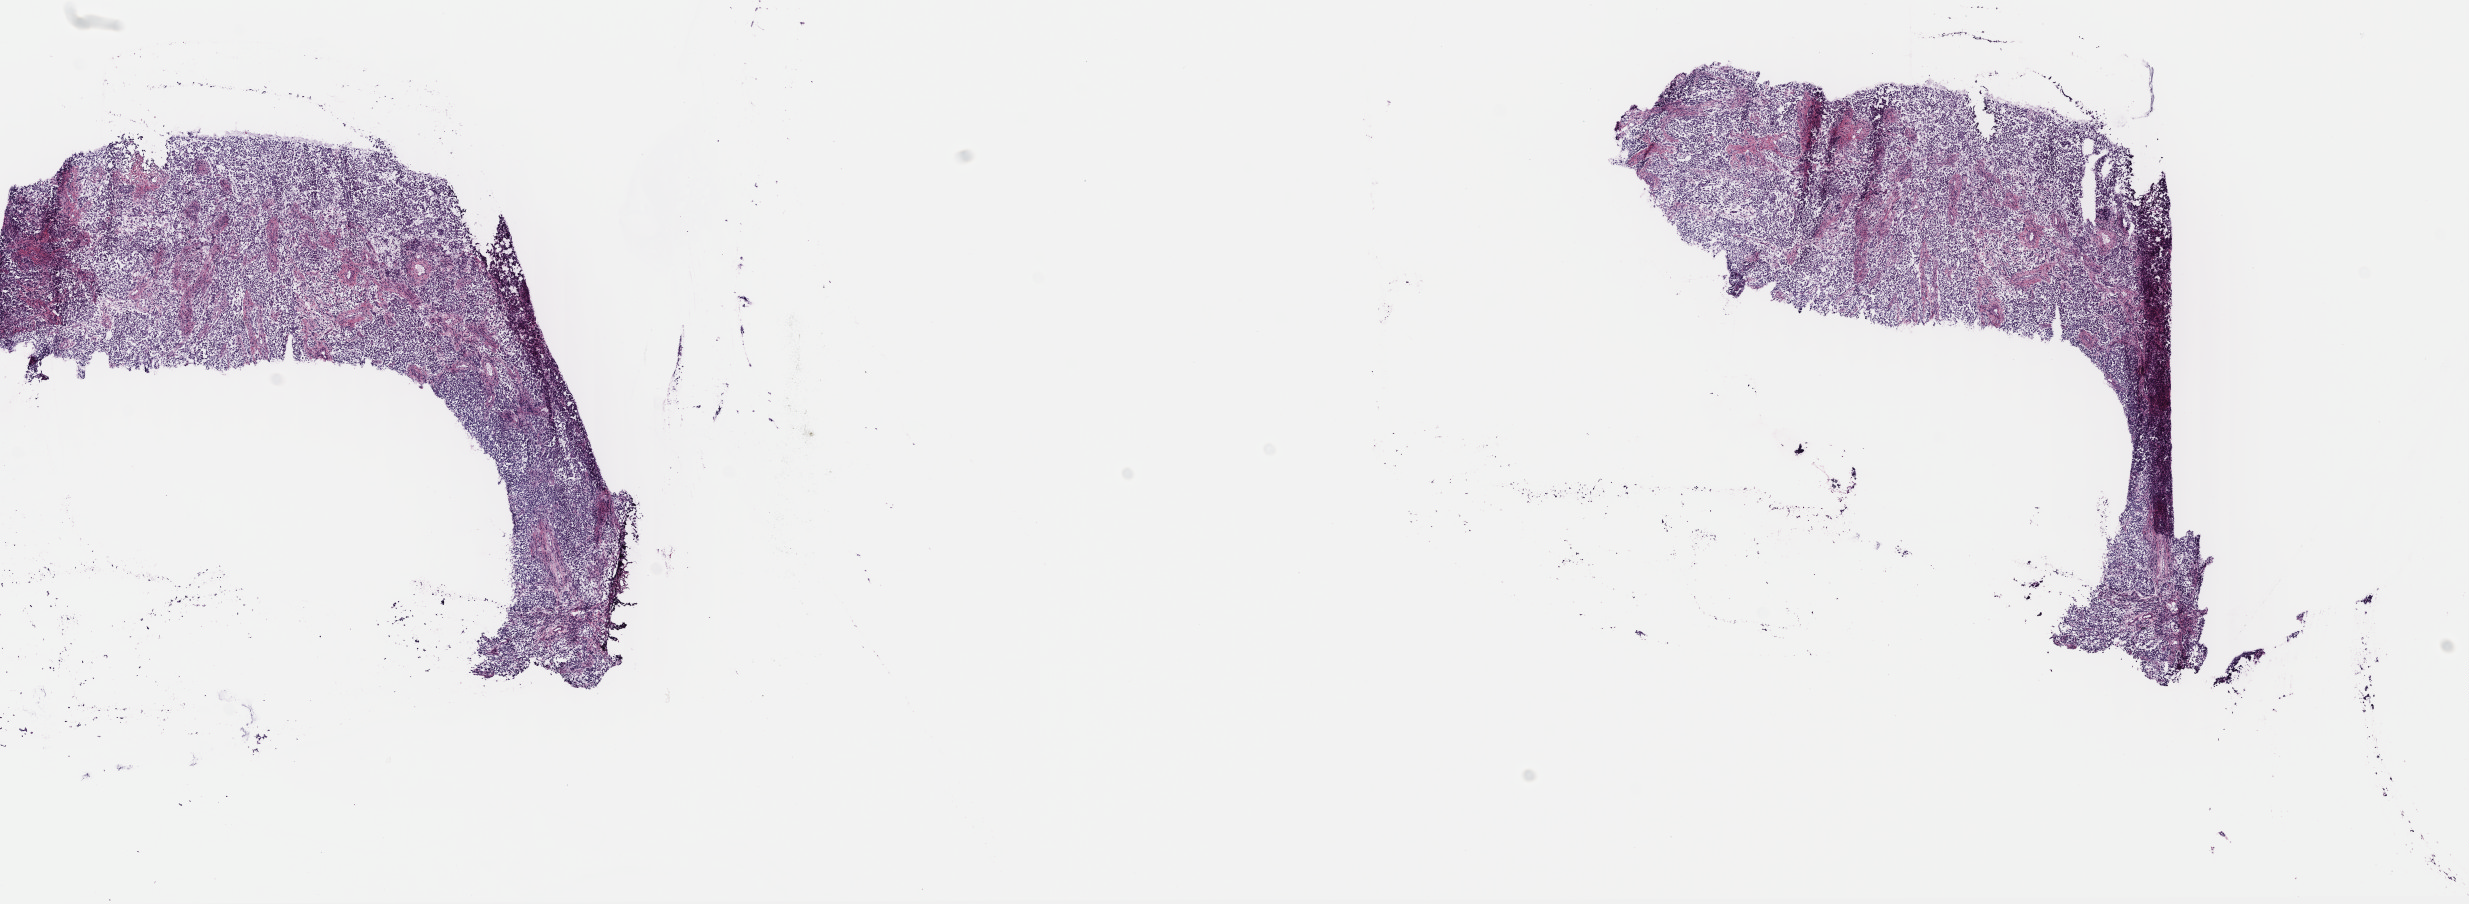
H&E whole-slide image, shown as a low-resolution overview of the whole scanned area (about 19.4 x 7.1 mm, from a 40x scan), frozen section from the top of the tissue portion, sample: primary tumour, cervix. Patient: female, age at initial diagnosis 34 years. Histologic grade: G3 (poorly differentiated). Slide review estimates, as recorded: tumour cells 80%, tumour nuclei 80%, normal cells 10%, stromal cells 5%, necrosis 5%. Inflammatory infiltration, as recorded: lymphocyte infiltration 4%, monocyte infiltration 1%, neutrophil infiltration 0%.
- histologic diagnosis: Squamous cell carcinoma, NOS (ovary)
- FIGO stage: IVB